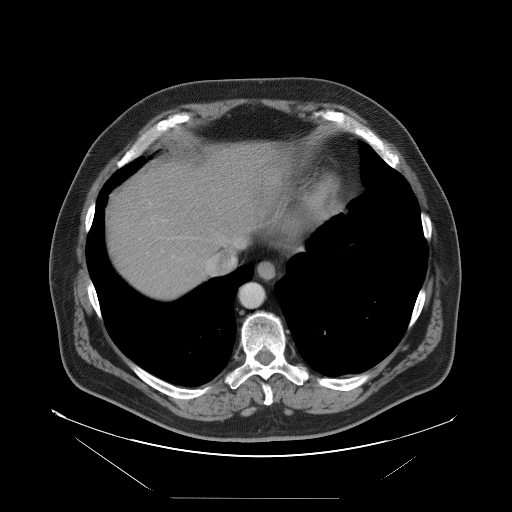
Contrast-enhanced abdominal CT, one axial slice; 120 kVp; intravenous contrast given; soft-tissue window (W 400 / L 40 HU); 512 × 512 image matrix, field of view 500 × 500 mm. Male patient, age 61 years. Case-level facts recorded for this patient, not image findings: diagnosis: colorectal cancer liver metastases, imaged before liver resection; multiple liver metastases: no; largest metastasis: 6.5 cm; disease in both lobes: yes.
Outlined on this slice (manually delineated by an expert):
- hepatic veins: box from (x=206, y=233) to (x=239, y=274) px
- liver: (x=107, y=143)–(x=285, y=298)
- planned liver remnant (the part of the liver to remain after resection): (x=159, y=144)–(x=286, y=253)